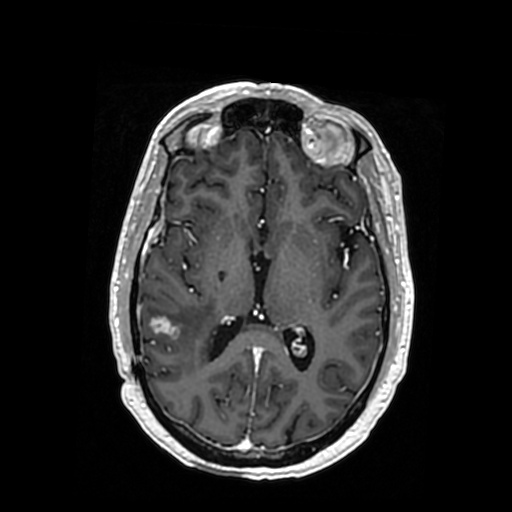
Brain MRI from a brain-tumour surgery series, one axial slice; T1-weighted post-contrast; 0.5 mm slice thickness; 512 × 512 image matrix. From the clinical record (not read from this slice): histopathology: Oligodendroglioma; WHO grade: 3.
Annotated regions visible in this slice (expert manual segmentation):
- tumour: bounding box (x1, y1, x2, y2) in pixels: (146, 315, 217, 372)